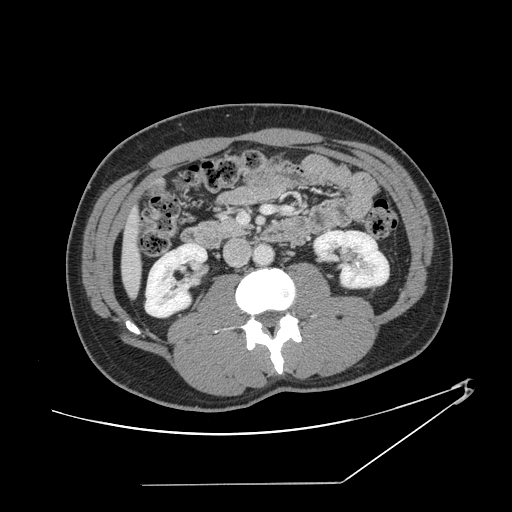
Contrast-enhanced abdominal CT, one axial slice; position 46 of 152 along the scan axis; reconstruction kernel STANDARD; soft-tissue window (W 400 / L 40 HU); 2.5 mm slice thickness; 512 × 512 image matrix. Male patient, age 45 years. From the clinical record (not read from this slice): diagnosis: colorectal cancer liver metastases, imaged before liver resection; multiple liver metastases: no; largest metastasis: 1 cm; disease in both lobes: no.
Outlined on this slice (manually delineated by an expert):
- liver: bounding box (x1, y1, x2, y2) in pixels: (124, 216, 141, 293)
- planned liver remnant (the part of the liver to remain after resection): (124, 216, 141, 294)
- portal vein (with intrahepatic branches): (239, 206, 292, 224)